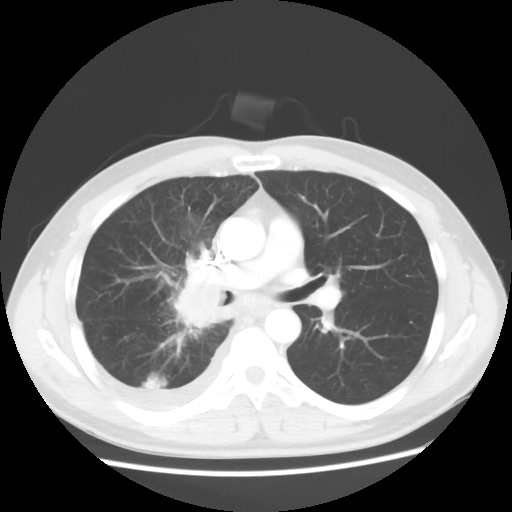
Chest CT, one axial slice; slice 31 of 56 in the series (ordered by position); reconstruction kernel STANDARD; 120 kVp; lung window (W 1500 / L -600 HU); 512 × 512 image matrix, field of view 360 × 360 mm. Male patient, age 46 years. From the clinical record (not read from this slice): clinical TNM (as recorded): T2 N3 M1.
Outlined on this slice (rectangle marked by the reading radiologist):
- lung tumour (recorded histology: adenocarcinoma): bounding box <161,253,229,336> (left, top, right, bottom; pixels)